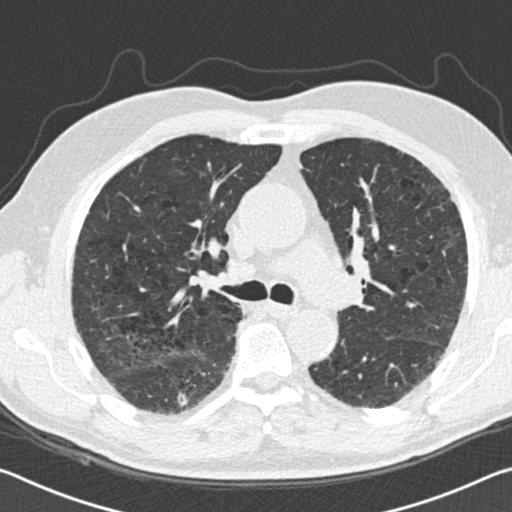
Axial slice from a low-dose chest CT screening exam. Second screening round (one year after baseline). Lung window (W 1500 / L -600 HU). 2 mm slice thickness. Standard (soft-tissue) reconstruction kernel (B30f). 120 kVp. Slice 56 of 142 in the series. 512 × 512 image matrix. Male, age 69 years at enrolment. Current smoker at enrolment.
• Expert reader's lesion annotation, bounding box (x1, y1, x2, y2) in pixels: (160, 377, 209, 424).
• Reader record for this screening exam (exam-level; its link to the box is not recorded): non-calcified nodule or mass ≥4 mm, right lower lobe, 10 × 10 mm, spiculated (stellate) margins, soft tissue attenuation, pre-existing on the prior screen: yes; interval growth: yes.
• Official screen result: positive, other.
• Participant outcome: lung cancer diagnosed 290 days after this screen — squamous cell carcinoma, NOS, right lower lobe, moderately differentiated (G2), stage IA (AJCC 6th edition), 25 mm at pathology.